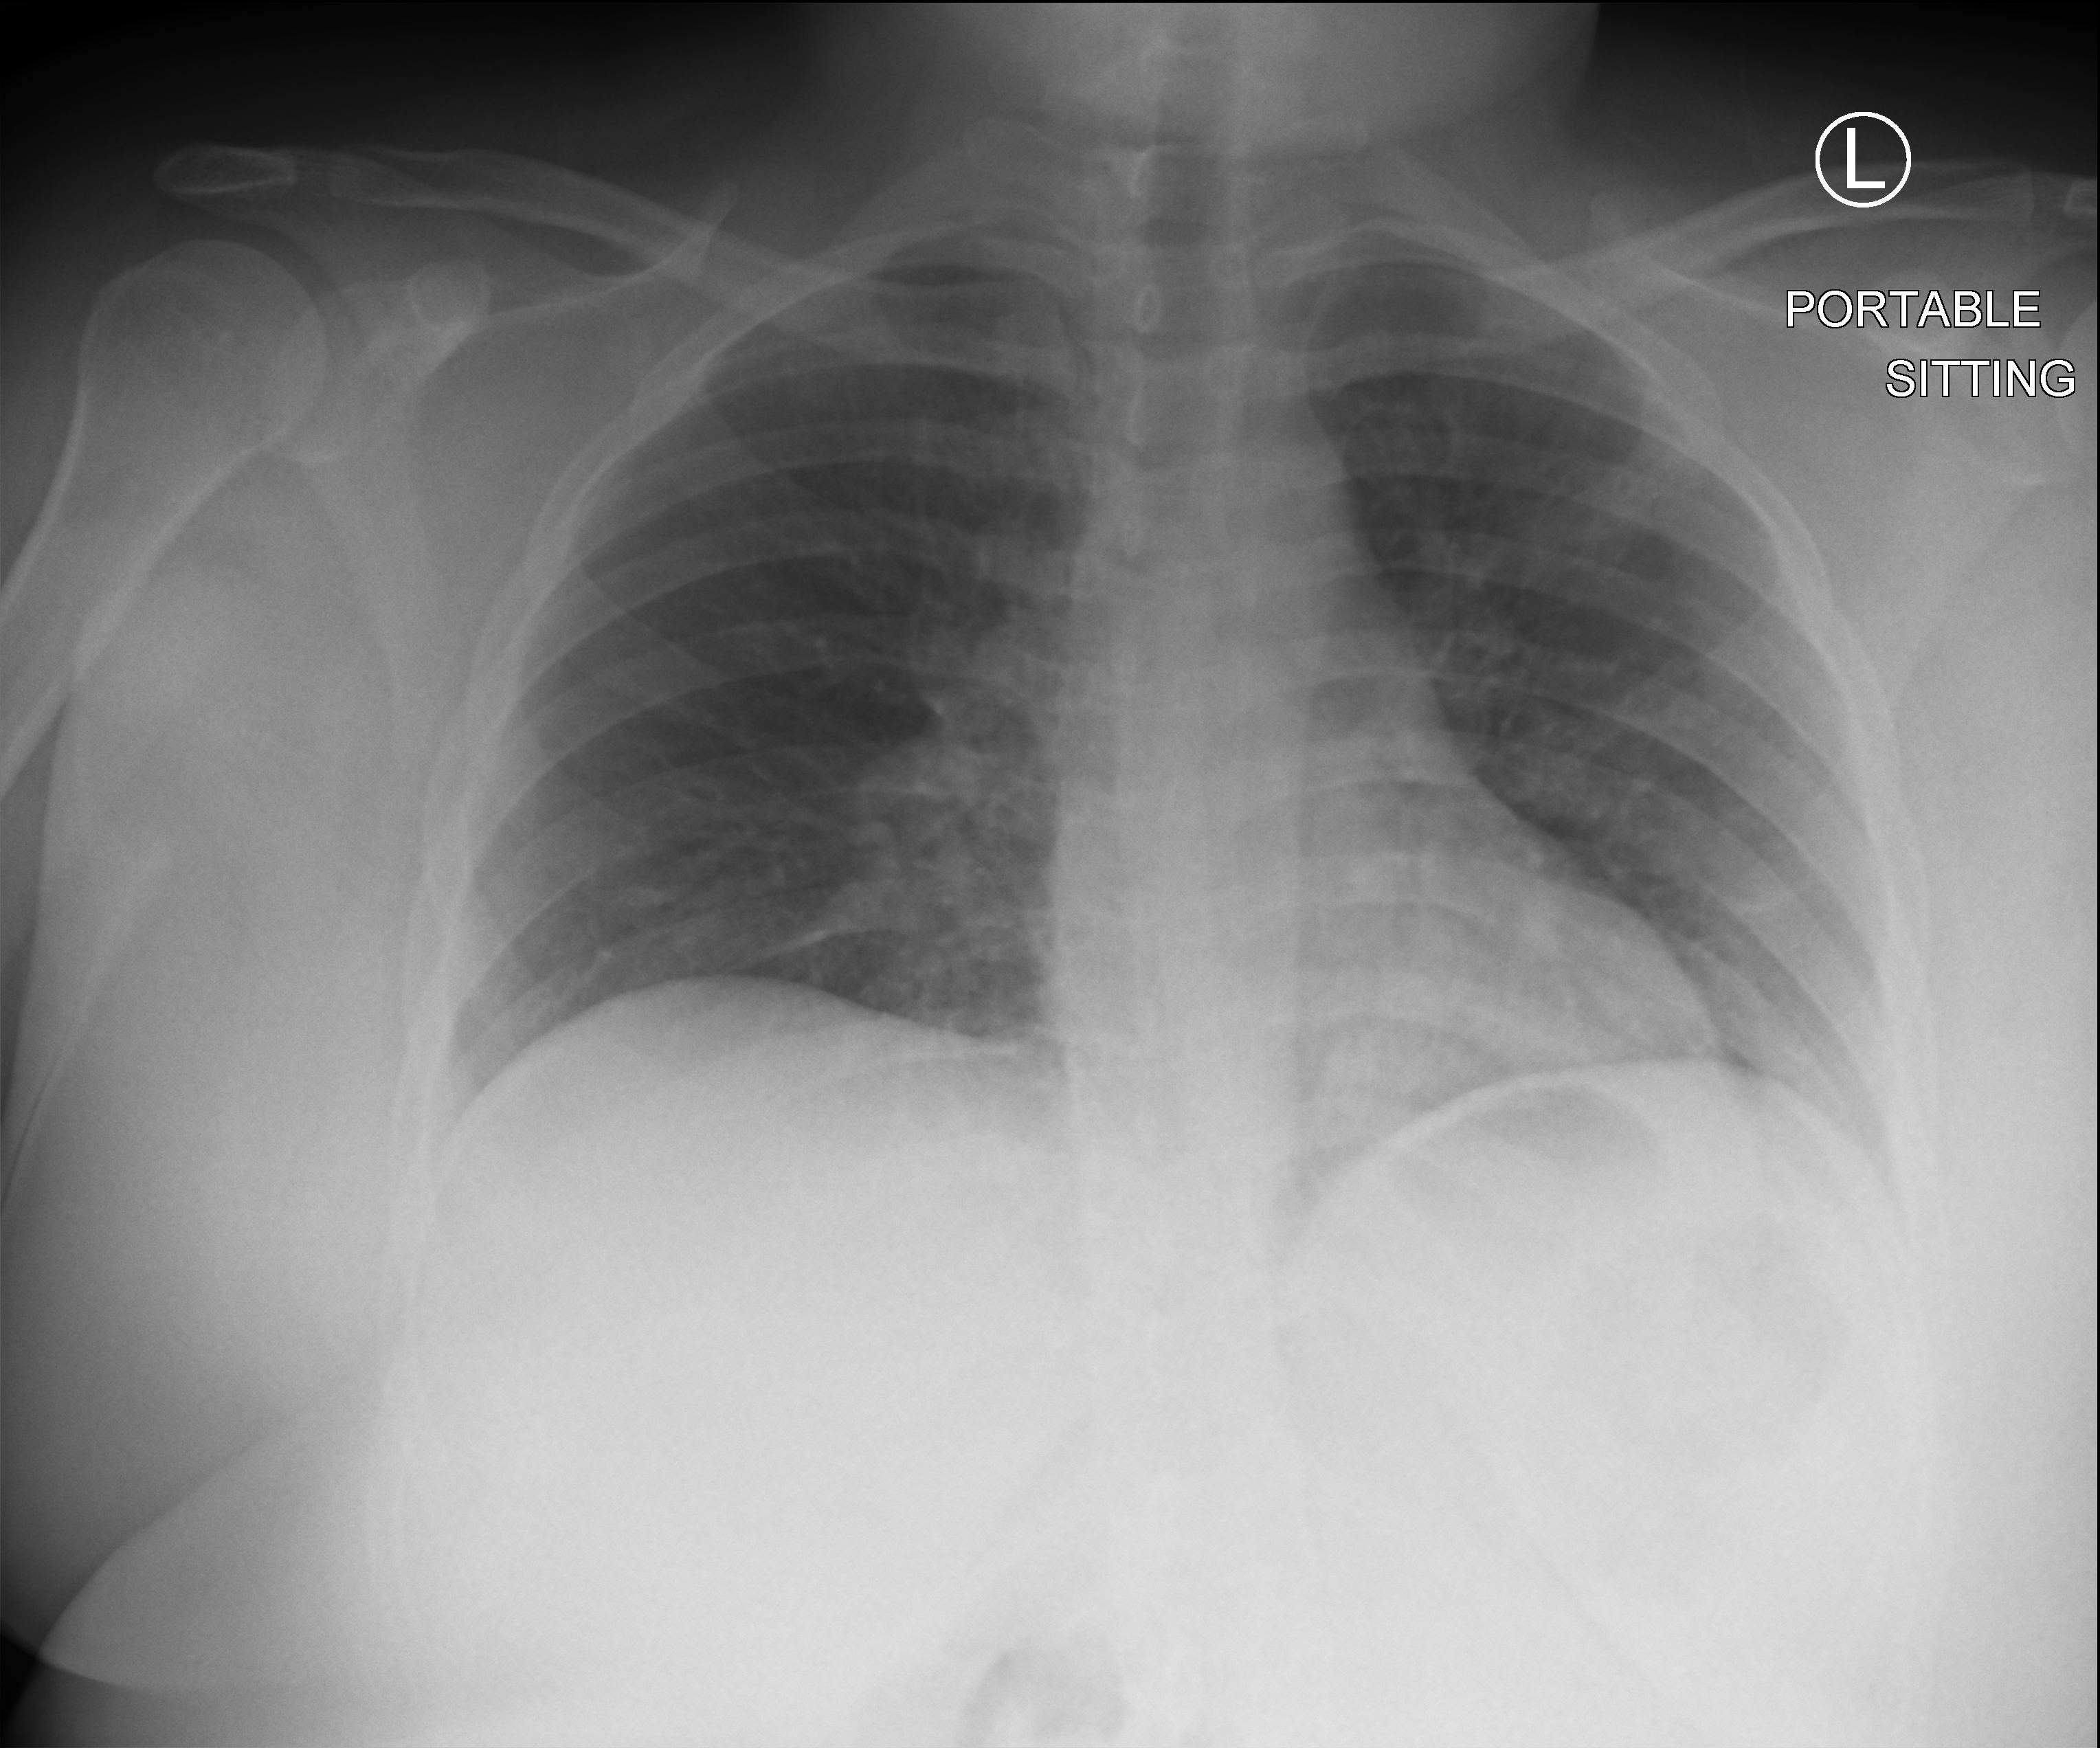
Bedside chest radiograph (computed radiography), anteroposterior (AP) projection. Patient hospitalised with COVID-19; female, aged 18–59 years.
Hospital-stay facts (about this admission, not read from this image; timing relative to this image not recorded): mechanically ventilated during this hospital stay: no; admitted to intensive care during this hospital stay: no.